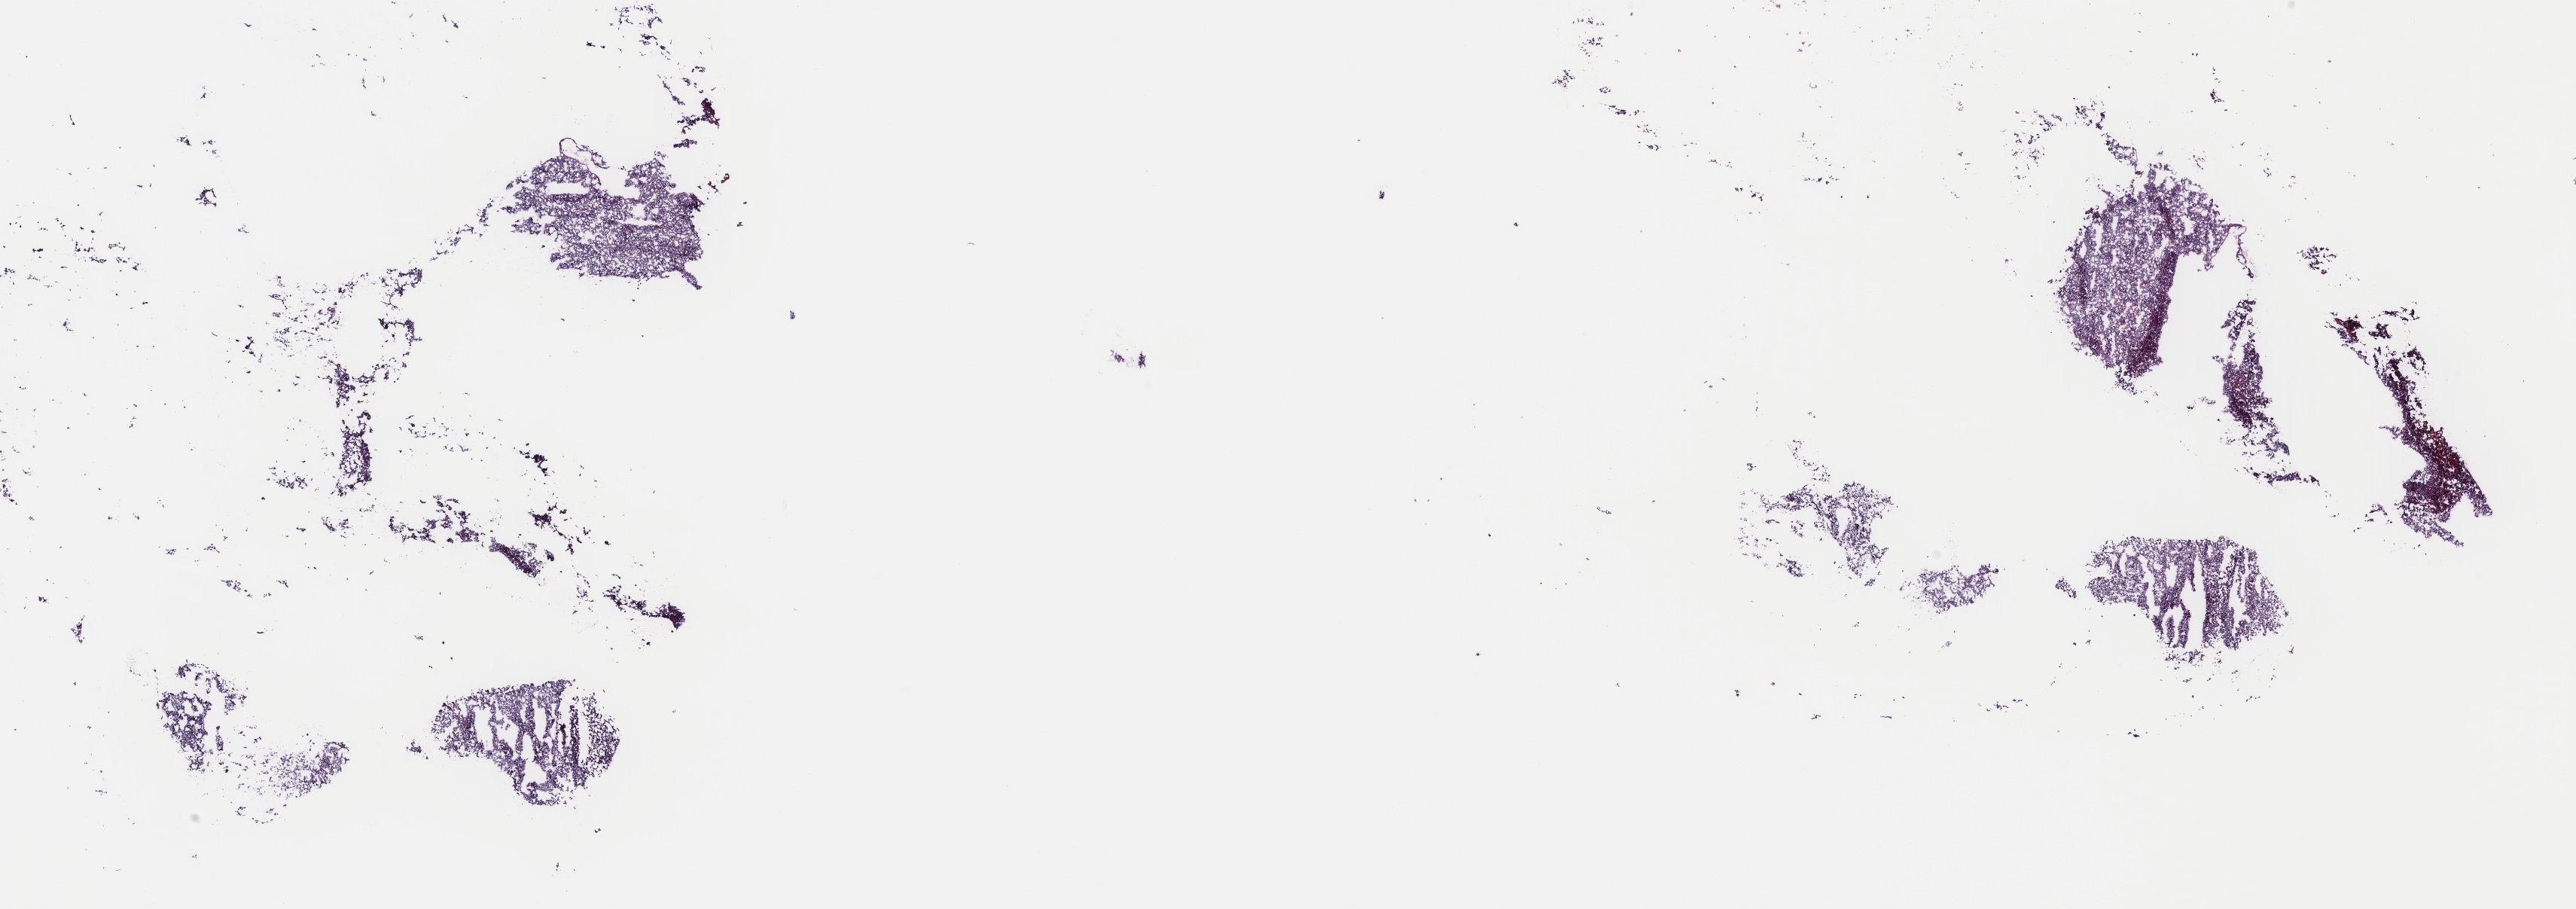
Digitized H&E tissue section (whole slide), whole scanned area (about 27.2 x 9.6 mm) shown as a low-resolution overview. Frozen section. Adrenal gland, primary tumour sample. Patient: female, age at initial diagnosis 43 years. Composition of this section per pathologist review: tumour cells 95%, tumour nuclei 95%, normal cells 0%, stromal cells 5%, necrosis 0%. Inflammatory infiltration, as recorded: lymphocyte infiltration 0%, monocyte infiltration 0%, neutrophil infiltration 0%.
Laterality: left. Diagnosis: Pheochromocytoma, NOS.